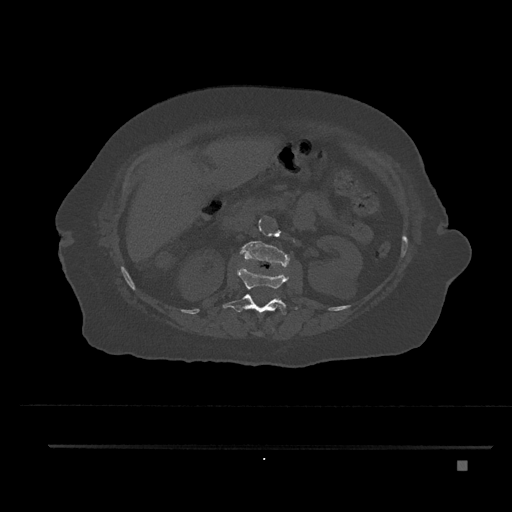
CT including the spine, one axial slice; slice 213 of 797 in the series (ordered by position); reconstruction kernel Br40s/3; bone window (W 1800 / L 400 HU); 512 × 512 image matrix, field of view 437 × 437 mm. Patient: female, 76 years. Case-level facts recorded for this patient, not image findings: primary cancer: lung; vertebrae with lytic lesions (as recorded): T11, L3.
Structures marked on this image (semi-automatically segmented with operator editing):
- L1 vertebra: bounding box <223,266,298,317> (left, top, right, bottom; pixels)
- L2 vertebra: <240,241,290,267>